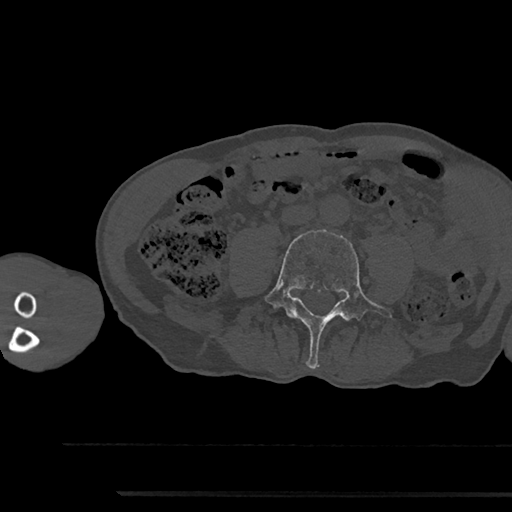
CT including the spine, one axial slice; position 417 of 797 along the scan axis; reconstruction kernel Br40s/3; 120 kVp; bone window (W 1800 / L 400 HU); 0.5 mm slice thickness; 512 × 512 image matrix. Male patient, age 79 years. From the clinical record (not read from this slice): primary cancer: prostate.
Structures marked on this image (semi-automatic segmentation, software-assisted and operator-edited):
- L4 vertebra: bounding box <264,230,392,369> (left, top, right, bottom; pixels)